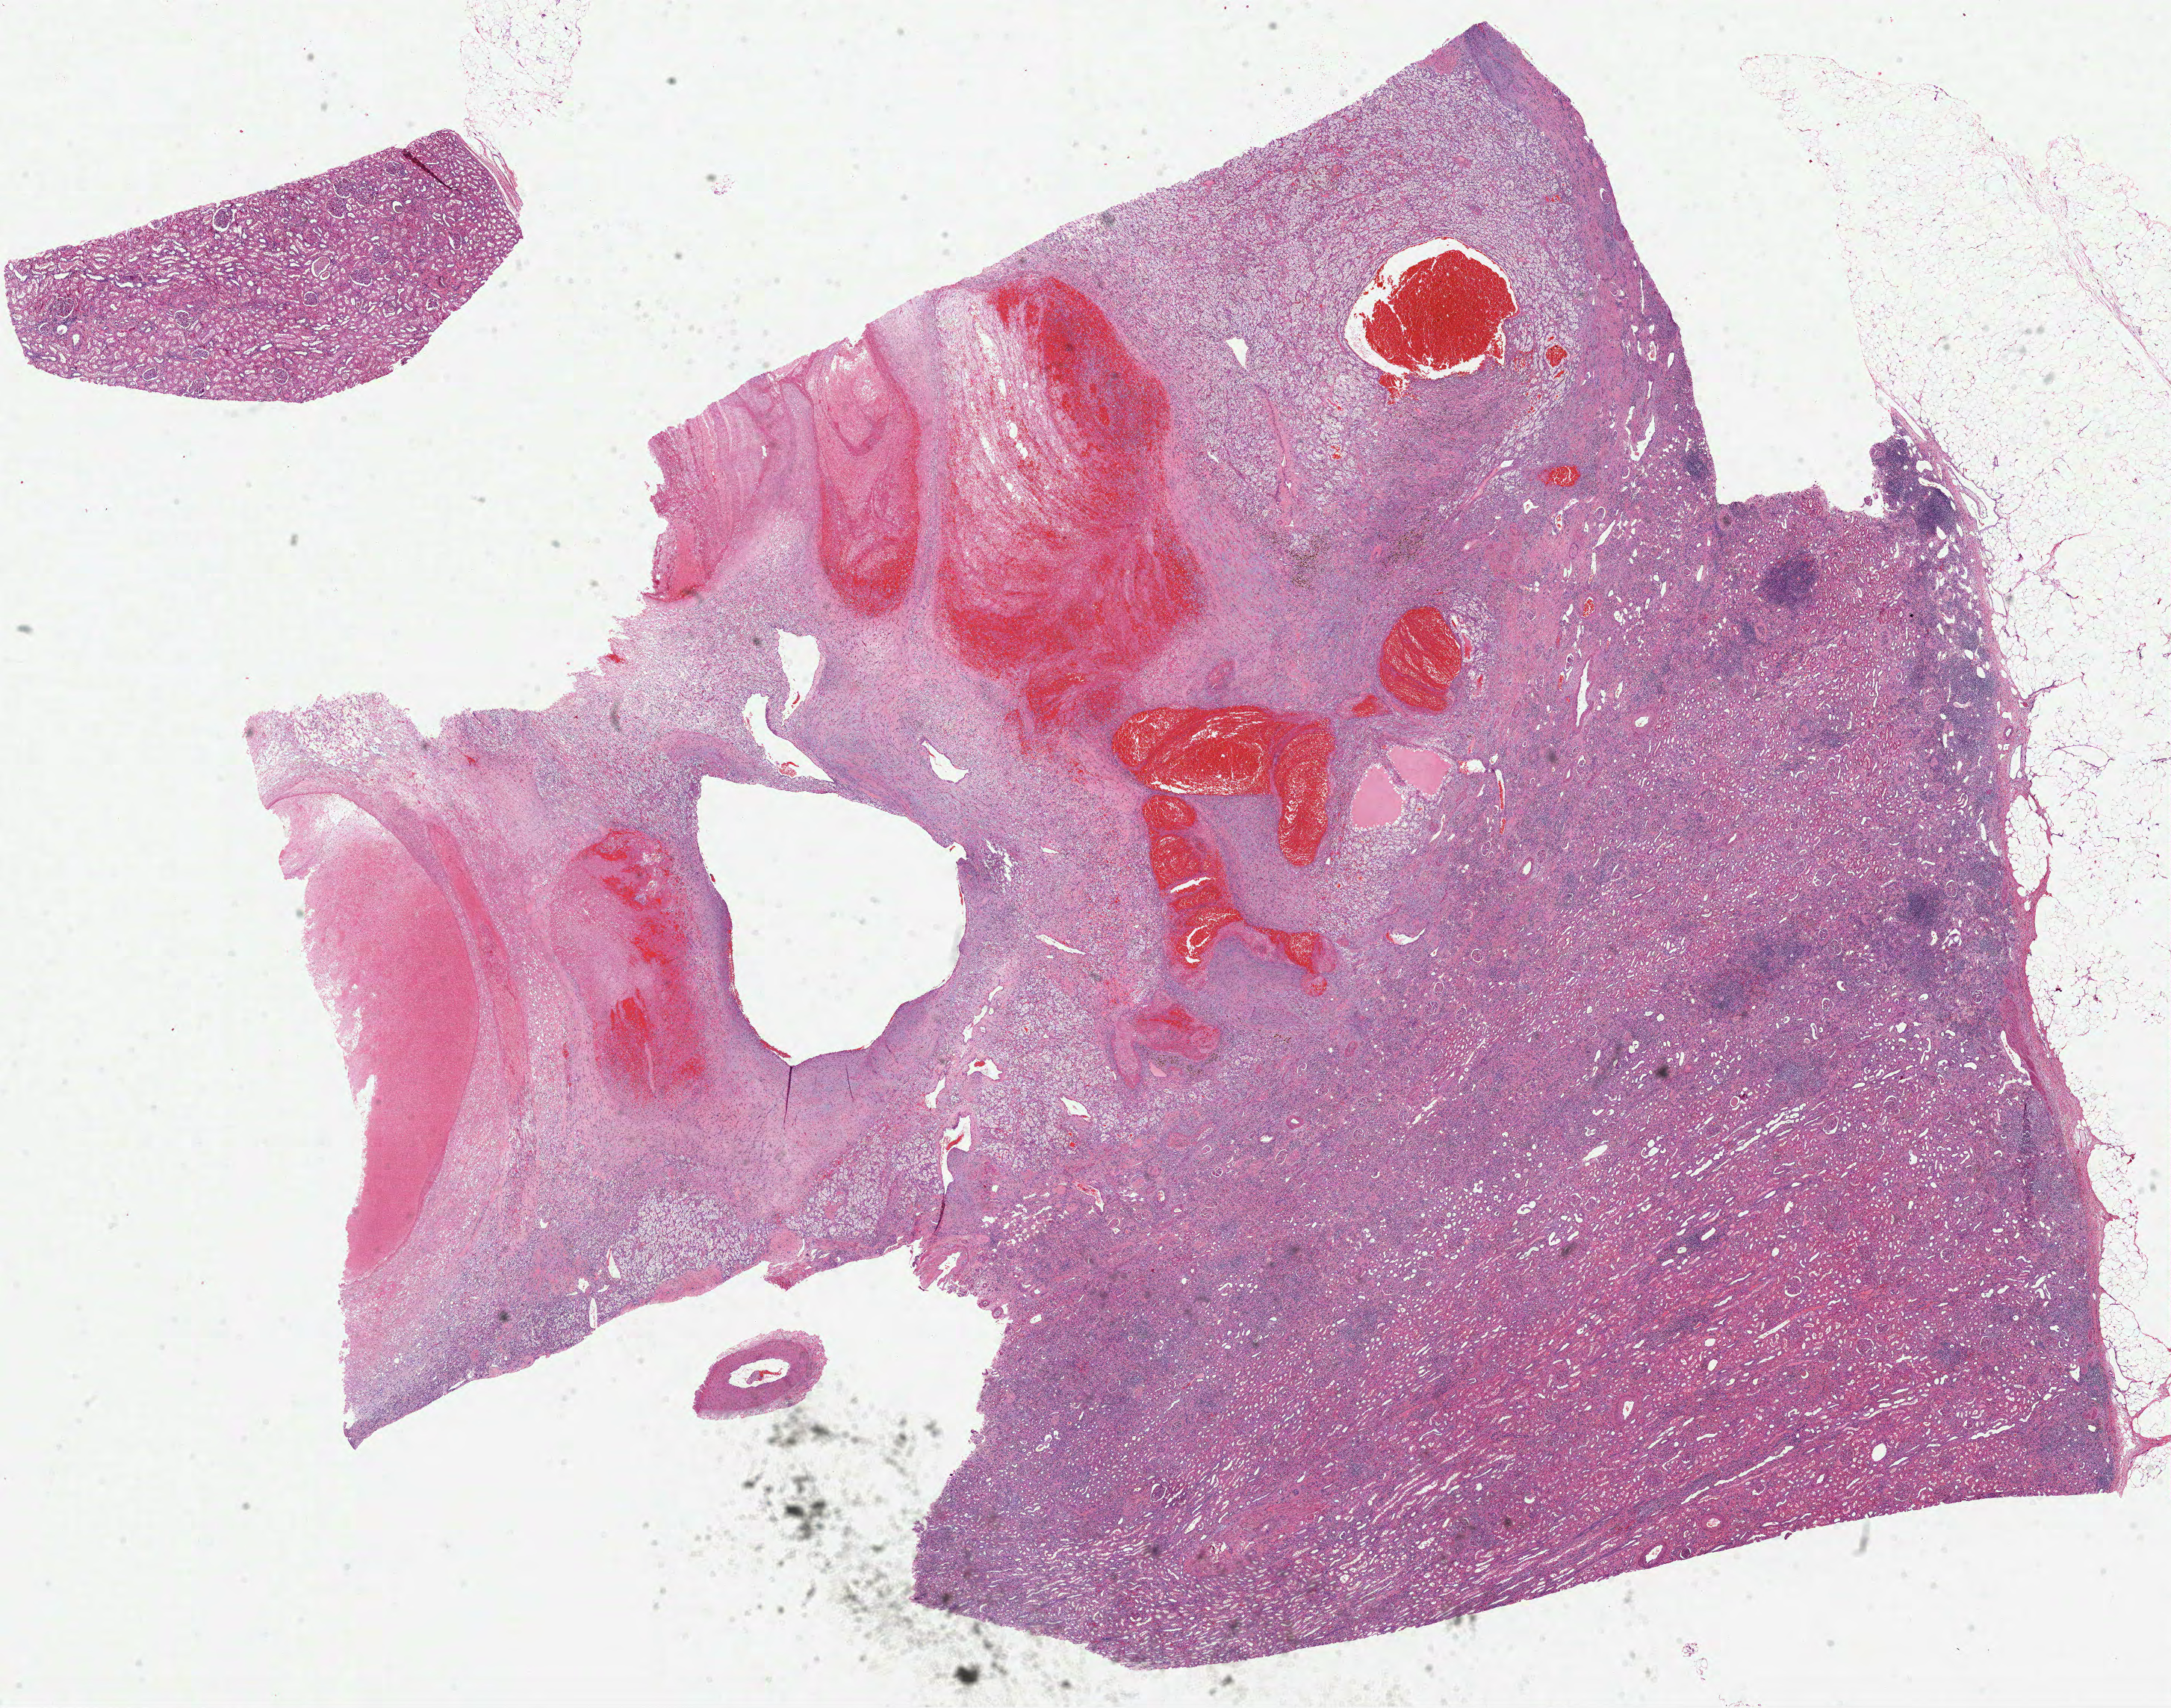
Whole-slide histology image, H&E — low-resolution overview of the scanned area, about 23.4 x 18.4 mm (from a 40x scan). FFPE section. Primary tumour sample from the kidney. Male patient; age at initial diagnosis 54 years. Histologic grade: G2 (moderately differentiated).
AJCC pathologic stage: III (6th edition). TNM: T3a N0 M0. Diagnosis: Clear cell adenocarcinoma, NOS.